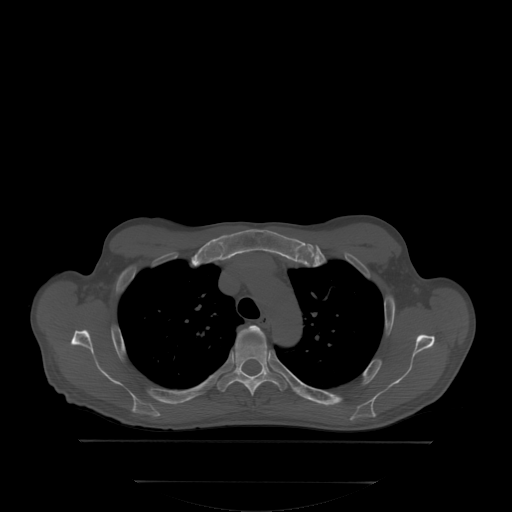
CT including the spine, one axial slice. Bone window (W 1800 / L 400 HU). 2.5 mm slice thickness. 512 × 512 image matrix, field of view 500 × 500 mm. Male patient, age 58 years. From the clinical record (not read from this slice): primary cancer: prostate; vertebrae with lytic lesions (as recorded): L1.
Annotated regions visible in this slice (semi-automatically segmented with operator editing):
- T3 vertebra: bounding box [x1, y1, x2, y2] px = [241, 326, 261, 336]
- T4 vertebra: [217, 331, 287, 394]